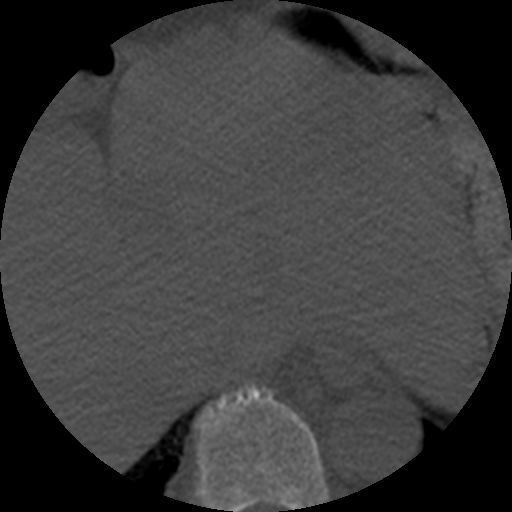
CT including the spine, one axial slice; slice 284 of 508 in the series (ordered by position); 120 kVp; bone window (W 1800 / L 400 HU); 1.25 mm slice thickness; 512 × 512 image matrix, field of view 160 × 160 mm. Patient age 57 years. From the clinical record (not read from this slice): primary cancer: prostate.
Structures marked on this image (semi-automatic segmentation, software-assisted and operator-edited):
- T9 vertebra: box from (x=196, y=384) to (x=329, y=512) px